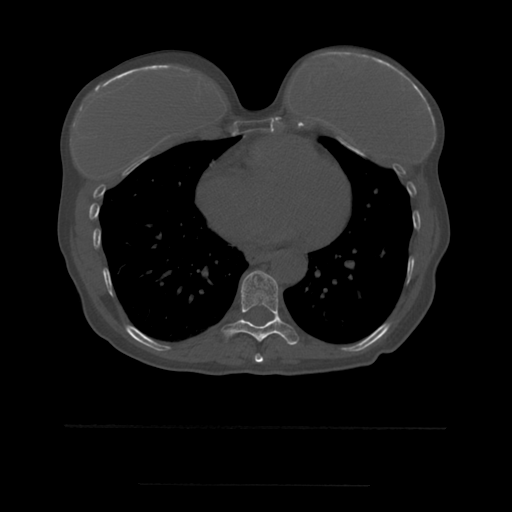
CT including the spine, one axial slice; slice 321 of 544 in the series (ordered by position); bone window (W 1800 / L 400 HU); 1.25 mm slice thickness; 512 × 512 image matrix, field of view 350 × 350 mm. Patient age 58 years. From the clinical record (not read from this slice): primary cancer: lung.
Structures marked on this image (semi-automatically segmented with operator editing):
- T8 vertebra: bounding box <255,354,264,363> (left, top, right, bottom; pixels)
- T9 vertebra: <222,271,299,345>